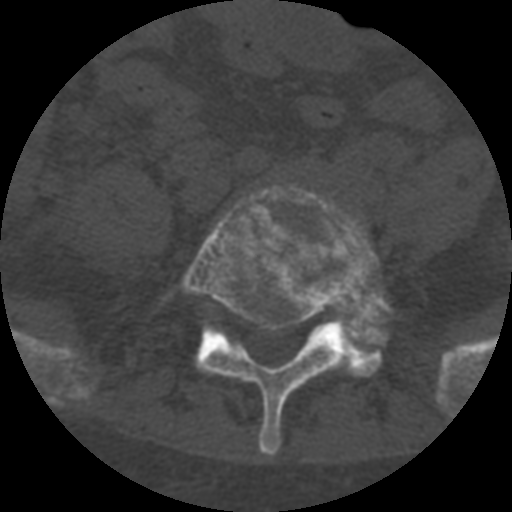
CT including the spine, one axial slice. Position 184 of 708 along the scan axis. Reconstruction kernel STANDARD. 120 kVp. One of 3 acquisitions stored at this slice position. Bone window (W 1800 / L 400 HU). 512 × 512 image matrix, field of view 160 × 160 mm. Patient age 55 years. Case-level facts recorded for this patient, not image findings: primary cancer: colon; vertebrae with lytic lesions (as recorded): T12, L1, L5.
Structures marked on this image (semi-automatically segmented with operator editing):
- L5 vertebra: bounding box (x1, y1, x2, y2) in pixels: (163, 185, 402, 456)